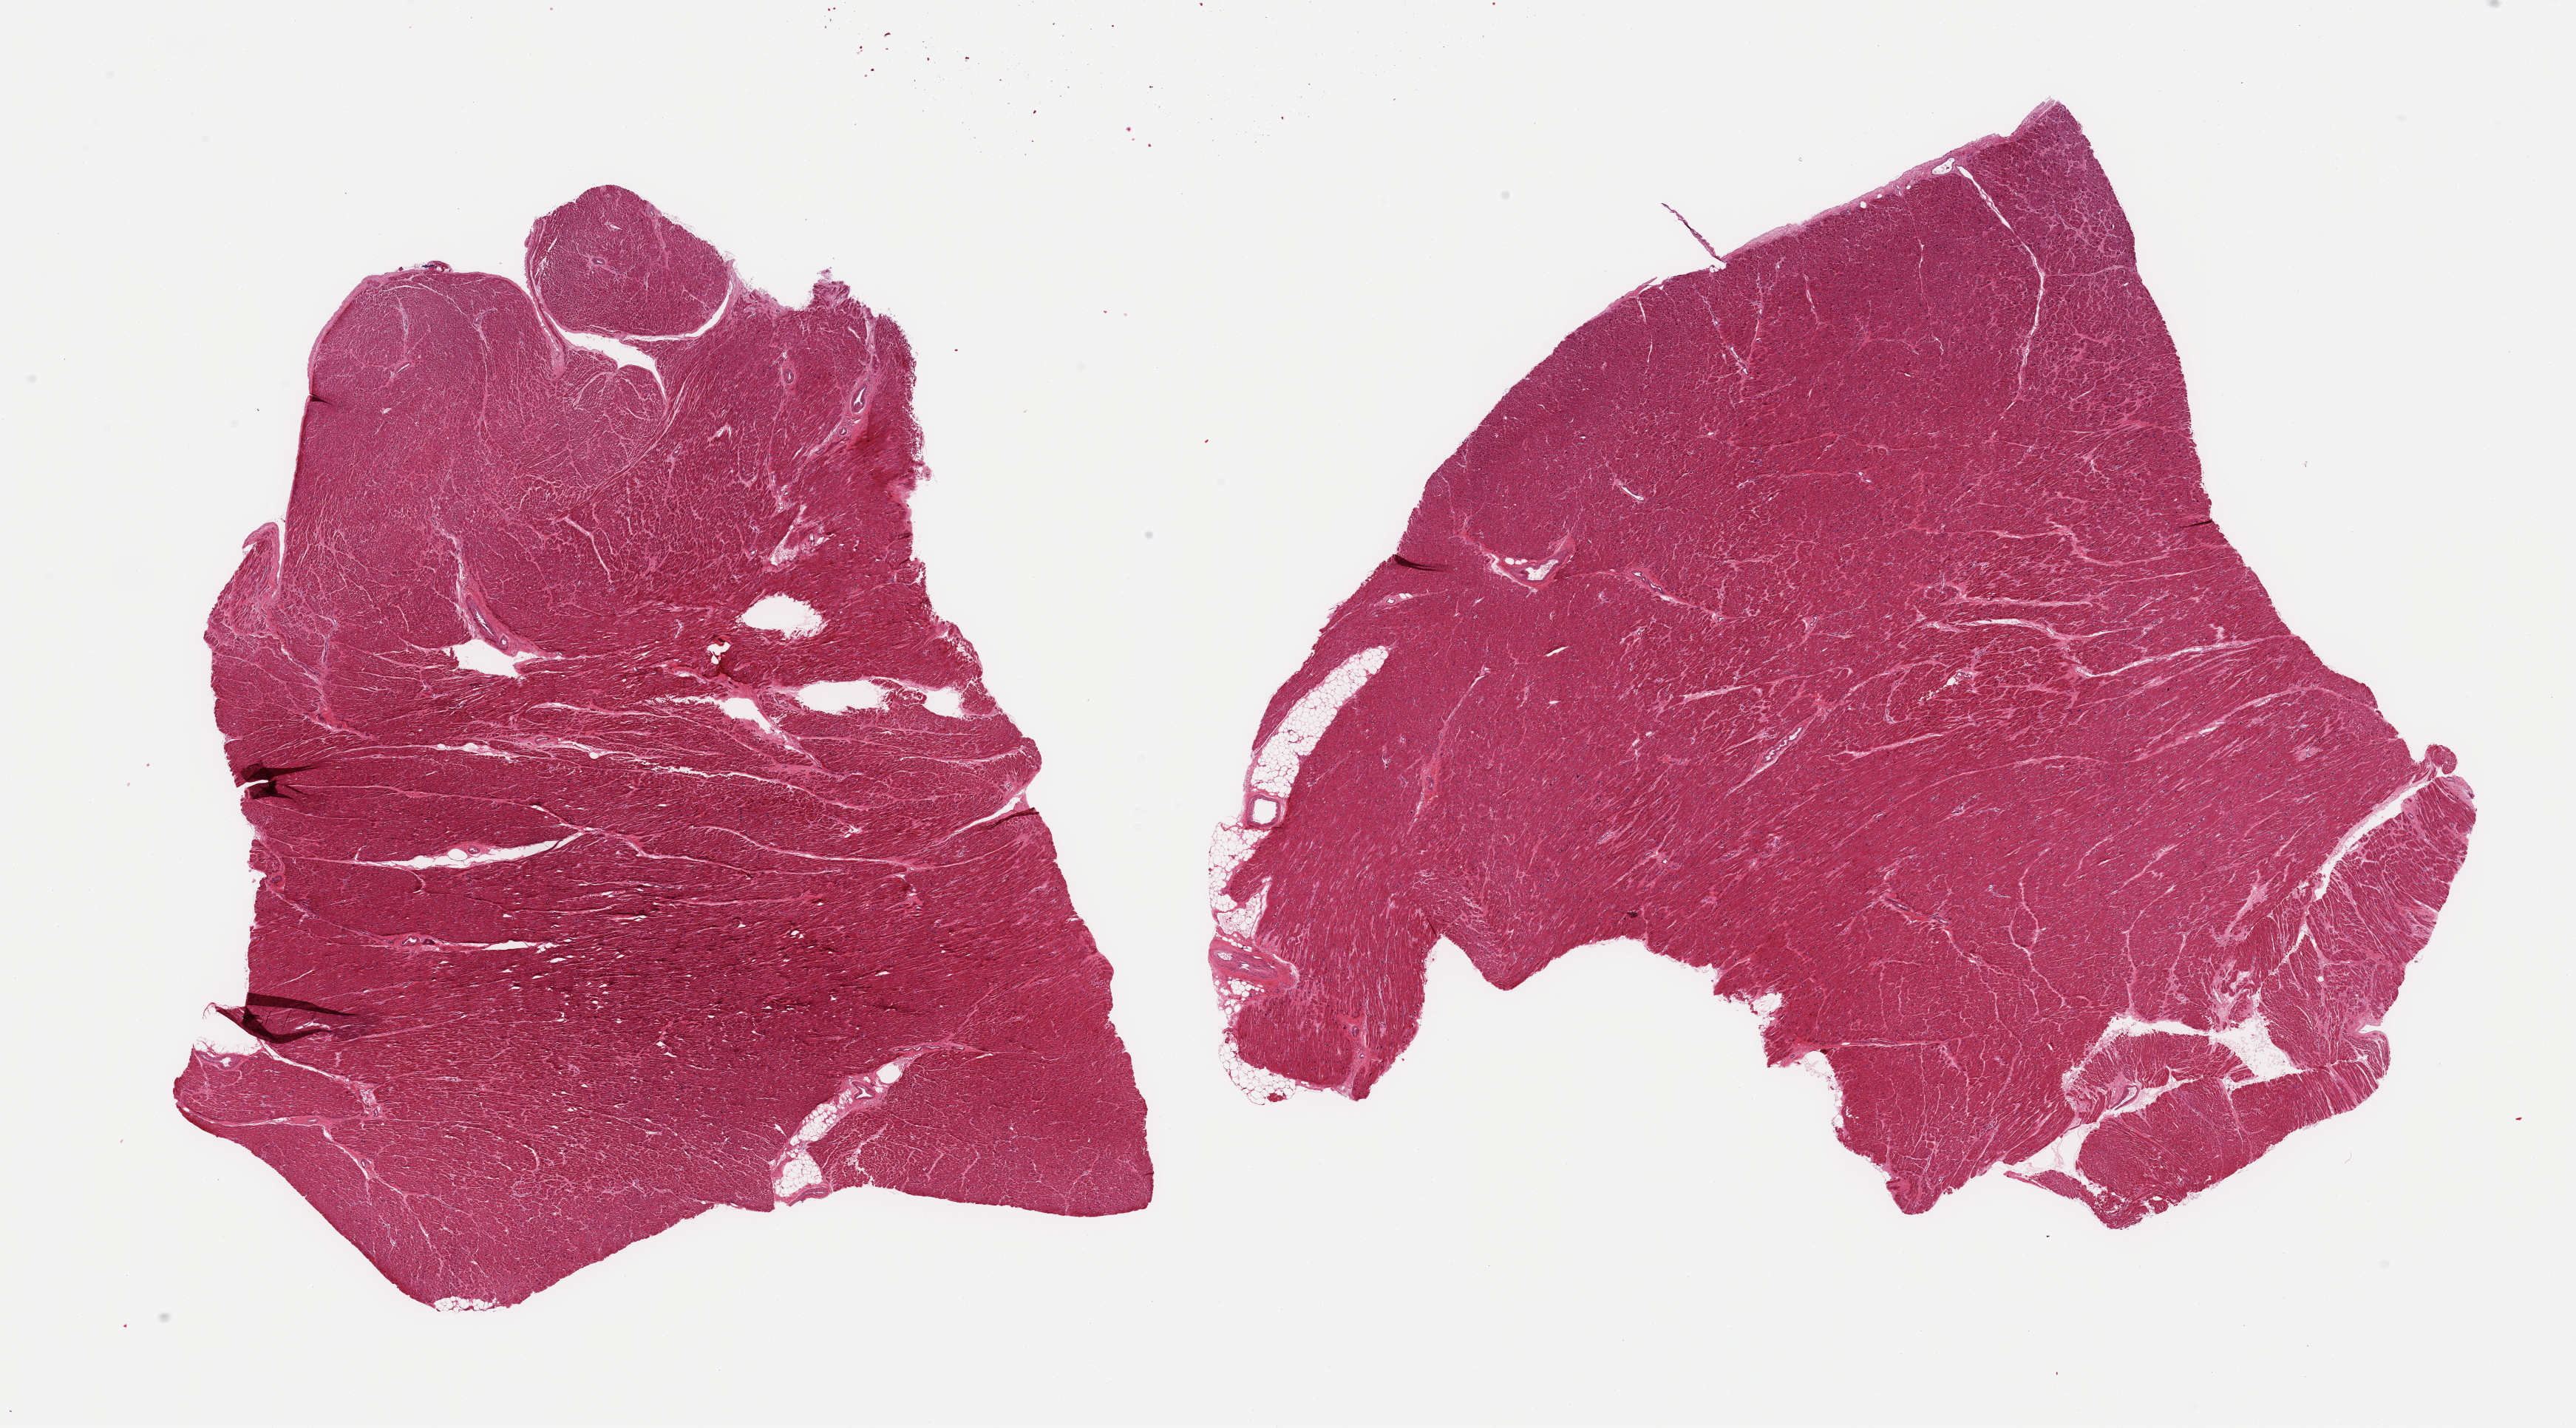
Haematoxylin and eosin whole-slide image, brightfield, shown as a low-resolution overview of the whole scanned area (about 27.6 x 15.3 mm, slide scanned at 20x), PAXgene-fixed, paraffin-embedded tissue, sampled site (target tissue): heart, donor tissue sample. Donor sex: male.
Review note (as recorded): 2 pieces; enlarged nuclei; <5% internal fat.